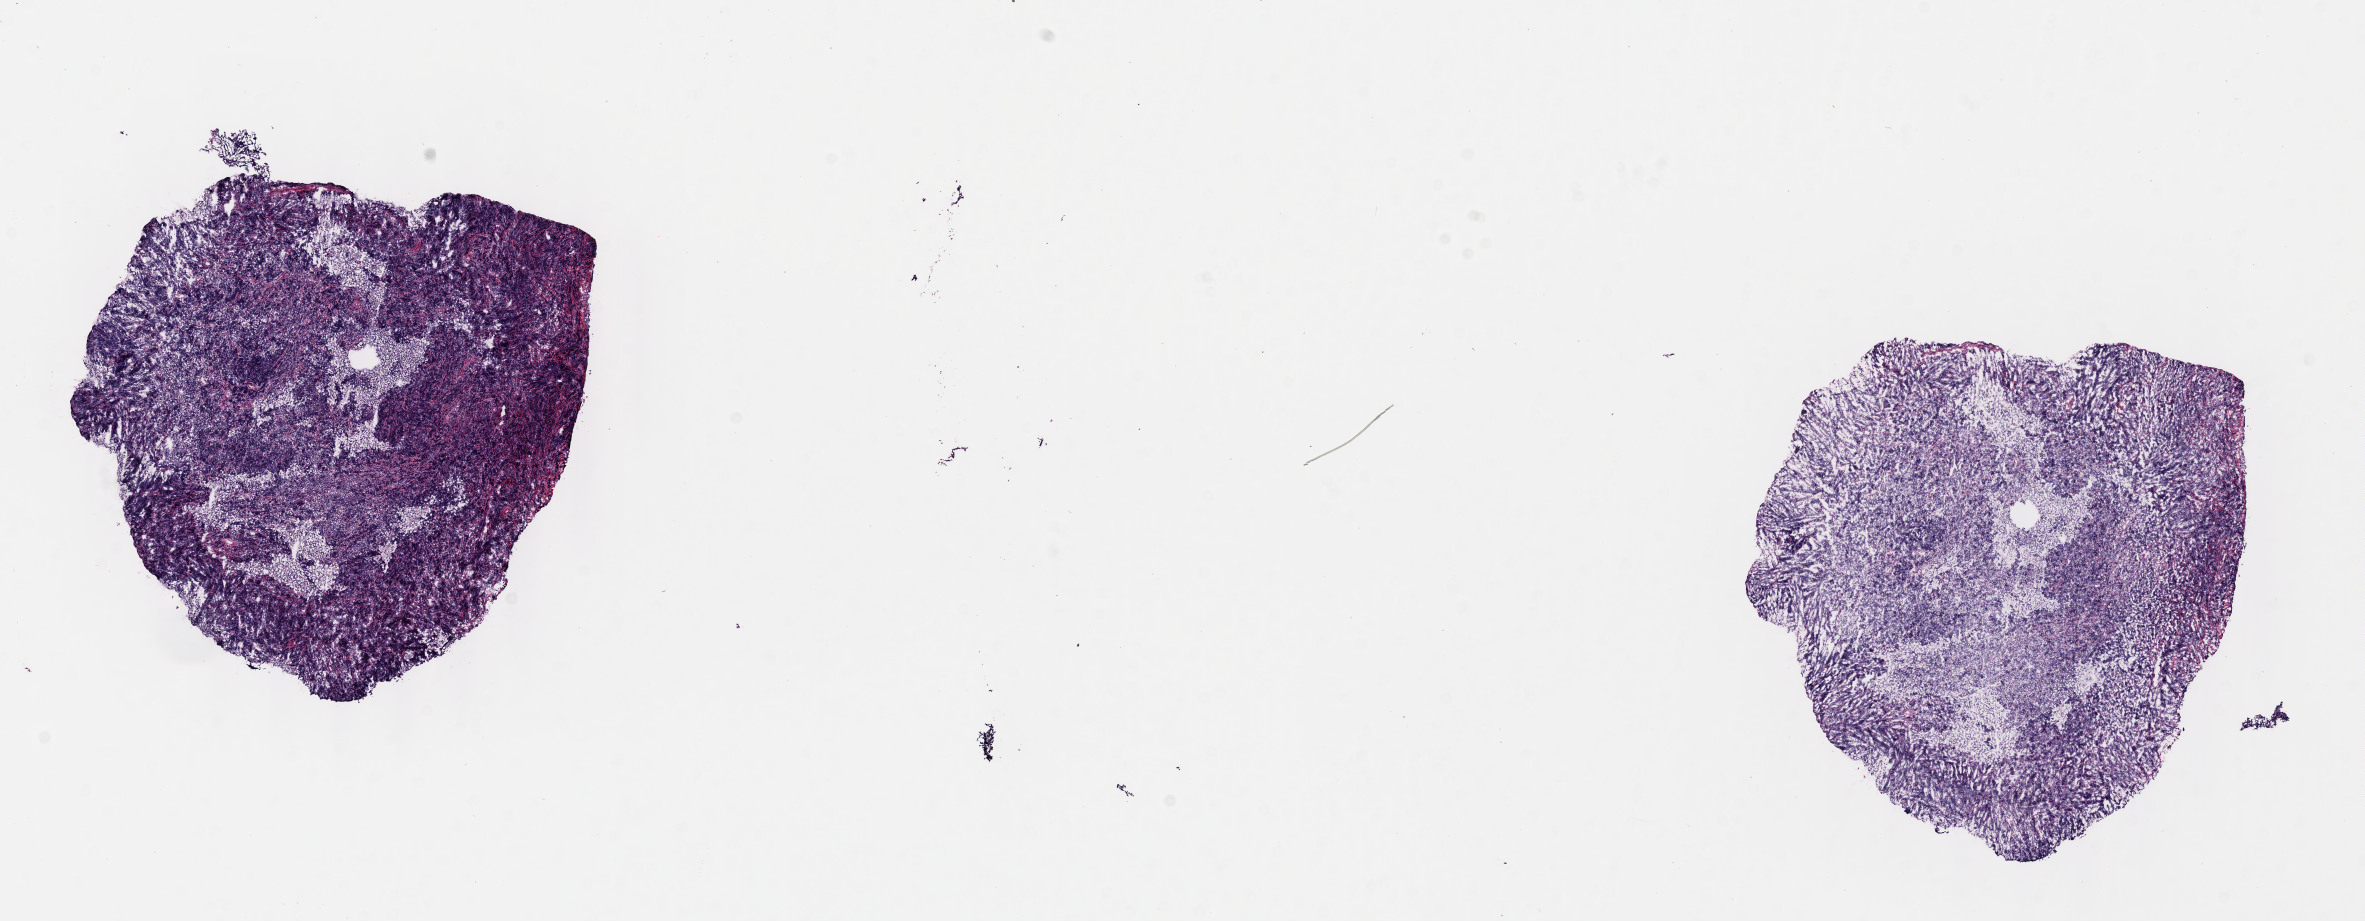
Whole-slide image, H&E stain — a low-resolution overview of the entire scanned area, about 19.1 x 7.4 mm, cryosection, primary tumor, site: mandible. Patient: male, age at initial diagnosis 9 years. Slide review estimates, as recorded: tumor cells 80%, tumor nuclei 80%.
Diagnosis: Burkitt lymphoma, NOS.